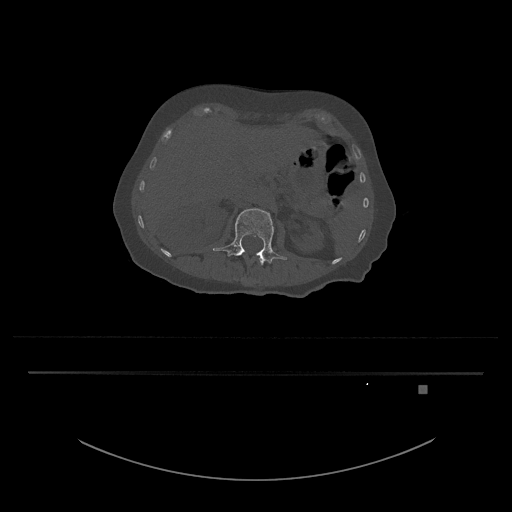
CT including the spine, one axial slice; position 501 of 797 along the scan axis; reconstruction kernel Br40s/3; bone window (W 1800 / L 400 HU); 512 × 512 image matrix. Patient: female, 57 years. From the clinical record (not read from this slice): primary cancer: cervical.
Structures marked on this image (semi-automatically segmented with operator editing):
- L1 vertebra: bounding box (x1, y1, x2, y2) in pixels: (257, 255, 265, 265)